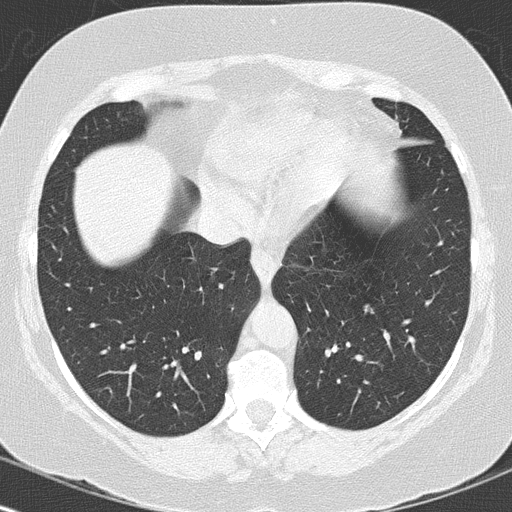
Low-dose screening chest CT, one axial slice; position 45 of 144 along the scan axis; reconstruction kernel B50f; 120 kVp; lung window (W 1500 / L -600 HU); 2 mm slice thickness; 512 × 512 image matrix.
Structures marked on this image (outlined manually by an expert reader):
- lesion 1 (tumor, lower lobe of left lung): bounding box (x1, y1, x2, y2) in pixels: (364, 305, 373, 313)